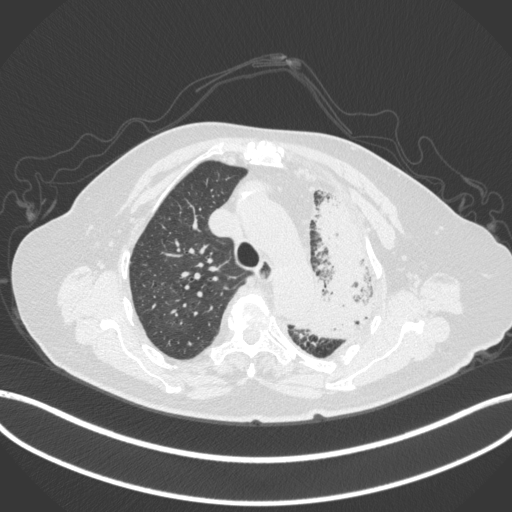
Chest CT, one axial slice; position 294 of 399 along the scan axis; reconstruction kernel B31f; lung window (W 1500 / L -600 HU); 1 mm slice thickness; 512 × 512 image matrix, field of view 400 × 400 mm. Female patient, age 75 years. From the clinical record (not read from this slice): clinical TNM (as recorded): T3 N3 M1.
Outlined on this slice (bounding box drawn by a radiologist):
- lung tumour (recorded histology: adenocarcinoma): bounding box <297,189,378,342> (left, top, right, bottom; pixels)